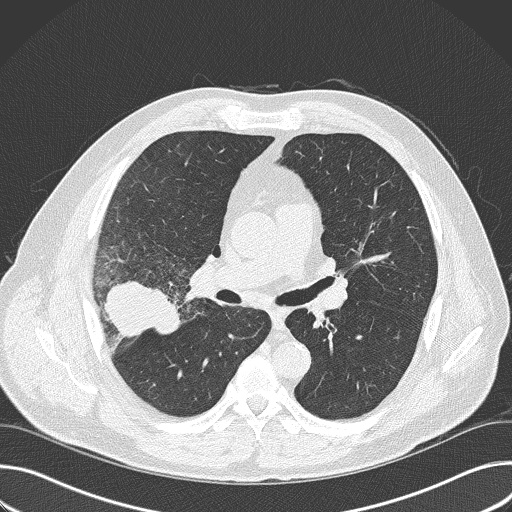
Low-dose screening chest CT, axial slice. First (baseline) screen. Lung window (W 1500 / L -600 HU). 2 mm slice thickness. Male, age 56 years at enrolment. Current smoker at enrolment.
Expert-annotated lung lesion, box from (x=80, y=257) to (x=183, y=361) px. Screening reader's record for this exam (one nodule recorded; not confirmed to be the boxed lesion): non-calcified nodule or mass ≥4 mm, right upper lobe, 6 × 5 mm, spiculated (stellate) margins, soft tissue attenuation.